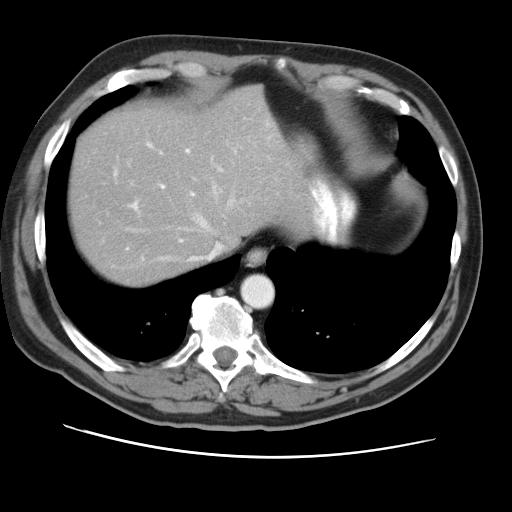
Contrast-enhanced abdominal CT, one axial slice. Slice 41 of 49 in the series (ordered by position). Reconstruction kernel STANDARD. Intravenous contrast given. Soft-tissue window (W 400 / L 40 HU). 5 mm slice thickness. 512 × 512 image matrix, field of view 374 × 374 mm. Male patient, age 59 years. Case-level facts recorded for this patient, not image findings: diagnosis: colorectal cancer liver metastases, imaged before liver resection; multiple liver metastases: yes; largest metastasis: 6.3 cm; disease in both lobes: yes.
Annotated regions visible in this slice (outlined manually by an expert reader):
- hepatic veins: bounding box [x1, y1, x2, y2] px = [126, 184, 232, 261]
- liver: [70, 87, 303, 284]
- planned liver remnant (the part of the liver to remain after resection): [70, 87, 303, 284]
- portal vein (with intrahepatic branches): [113, 143, 201, 259]